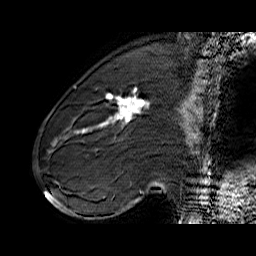
Breast MRI (dynamic contrast-enhanced), one sagittal slice. Slice 21 of 60 in the series (ordered by position). Dynamic contrast-enhanced series, time point 2 of 6 at this slice position (early post-contrast). 1.5 T. TE 6.4 ms, TR 32.9 ms. 4 mm slice thickness. 256 × 256 image matrix. Female patient. From the clinical record (not read from this slice): setting: breast cancer imaged before/during neoadjuvant chemotherapy; receptor status: HER2-positive.
Annotated regions visible in this slice (semi-automatic segmentation, software-assisted and operator-edited):
- analysis volume of interest (the breast-tissue region the enhancement analysis was run in; not a lesion): bounding box (x1, y1, x2, y2) in pixels: (71, 80, 155, 146)
- tumour enhancement mask (voxels above the 100 % enhancement threshold inside the analysis volume of interest): (76, 88, 149, 133)